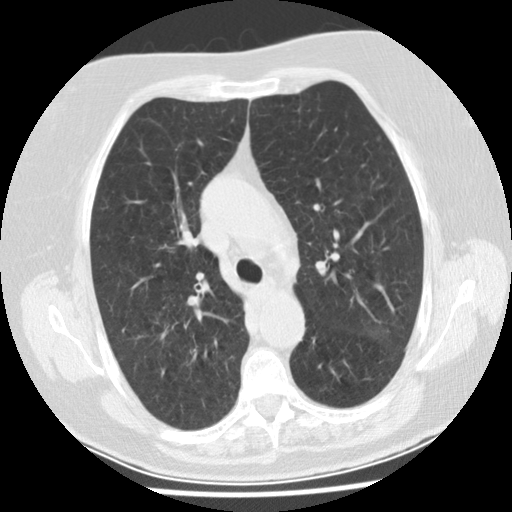
Chest CT (low-dose screening protocol), one axial image. First (baseline) screen. Lung window (W 1500 / L -600 HU). 2.5 mm slice thickness. Standard (soft-tissue) reconstruction kernel (STANDARD). Slice 107 of 149 in the series. Female participant, aged 74 years at enrolment. Former smoker at enrolment.
Expert-annotated lung lesion, bounding box [x1, y1, x2, y2] px = [342, 301, 411, 356]. The screening reader recorded 2 non-calcified nodules or masses ≥4 mm on this exam; which of them this box marks is not recorded.